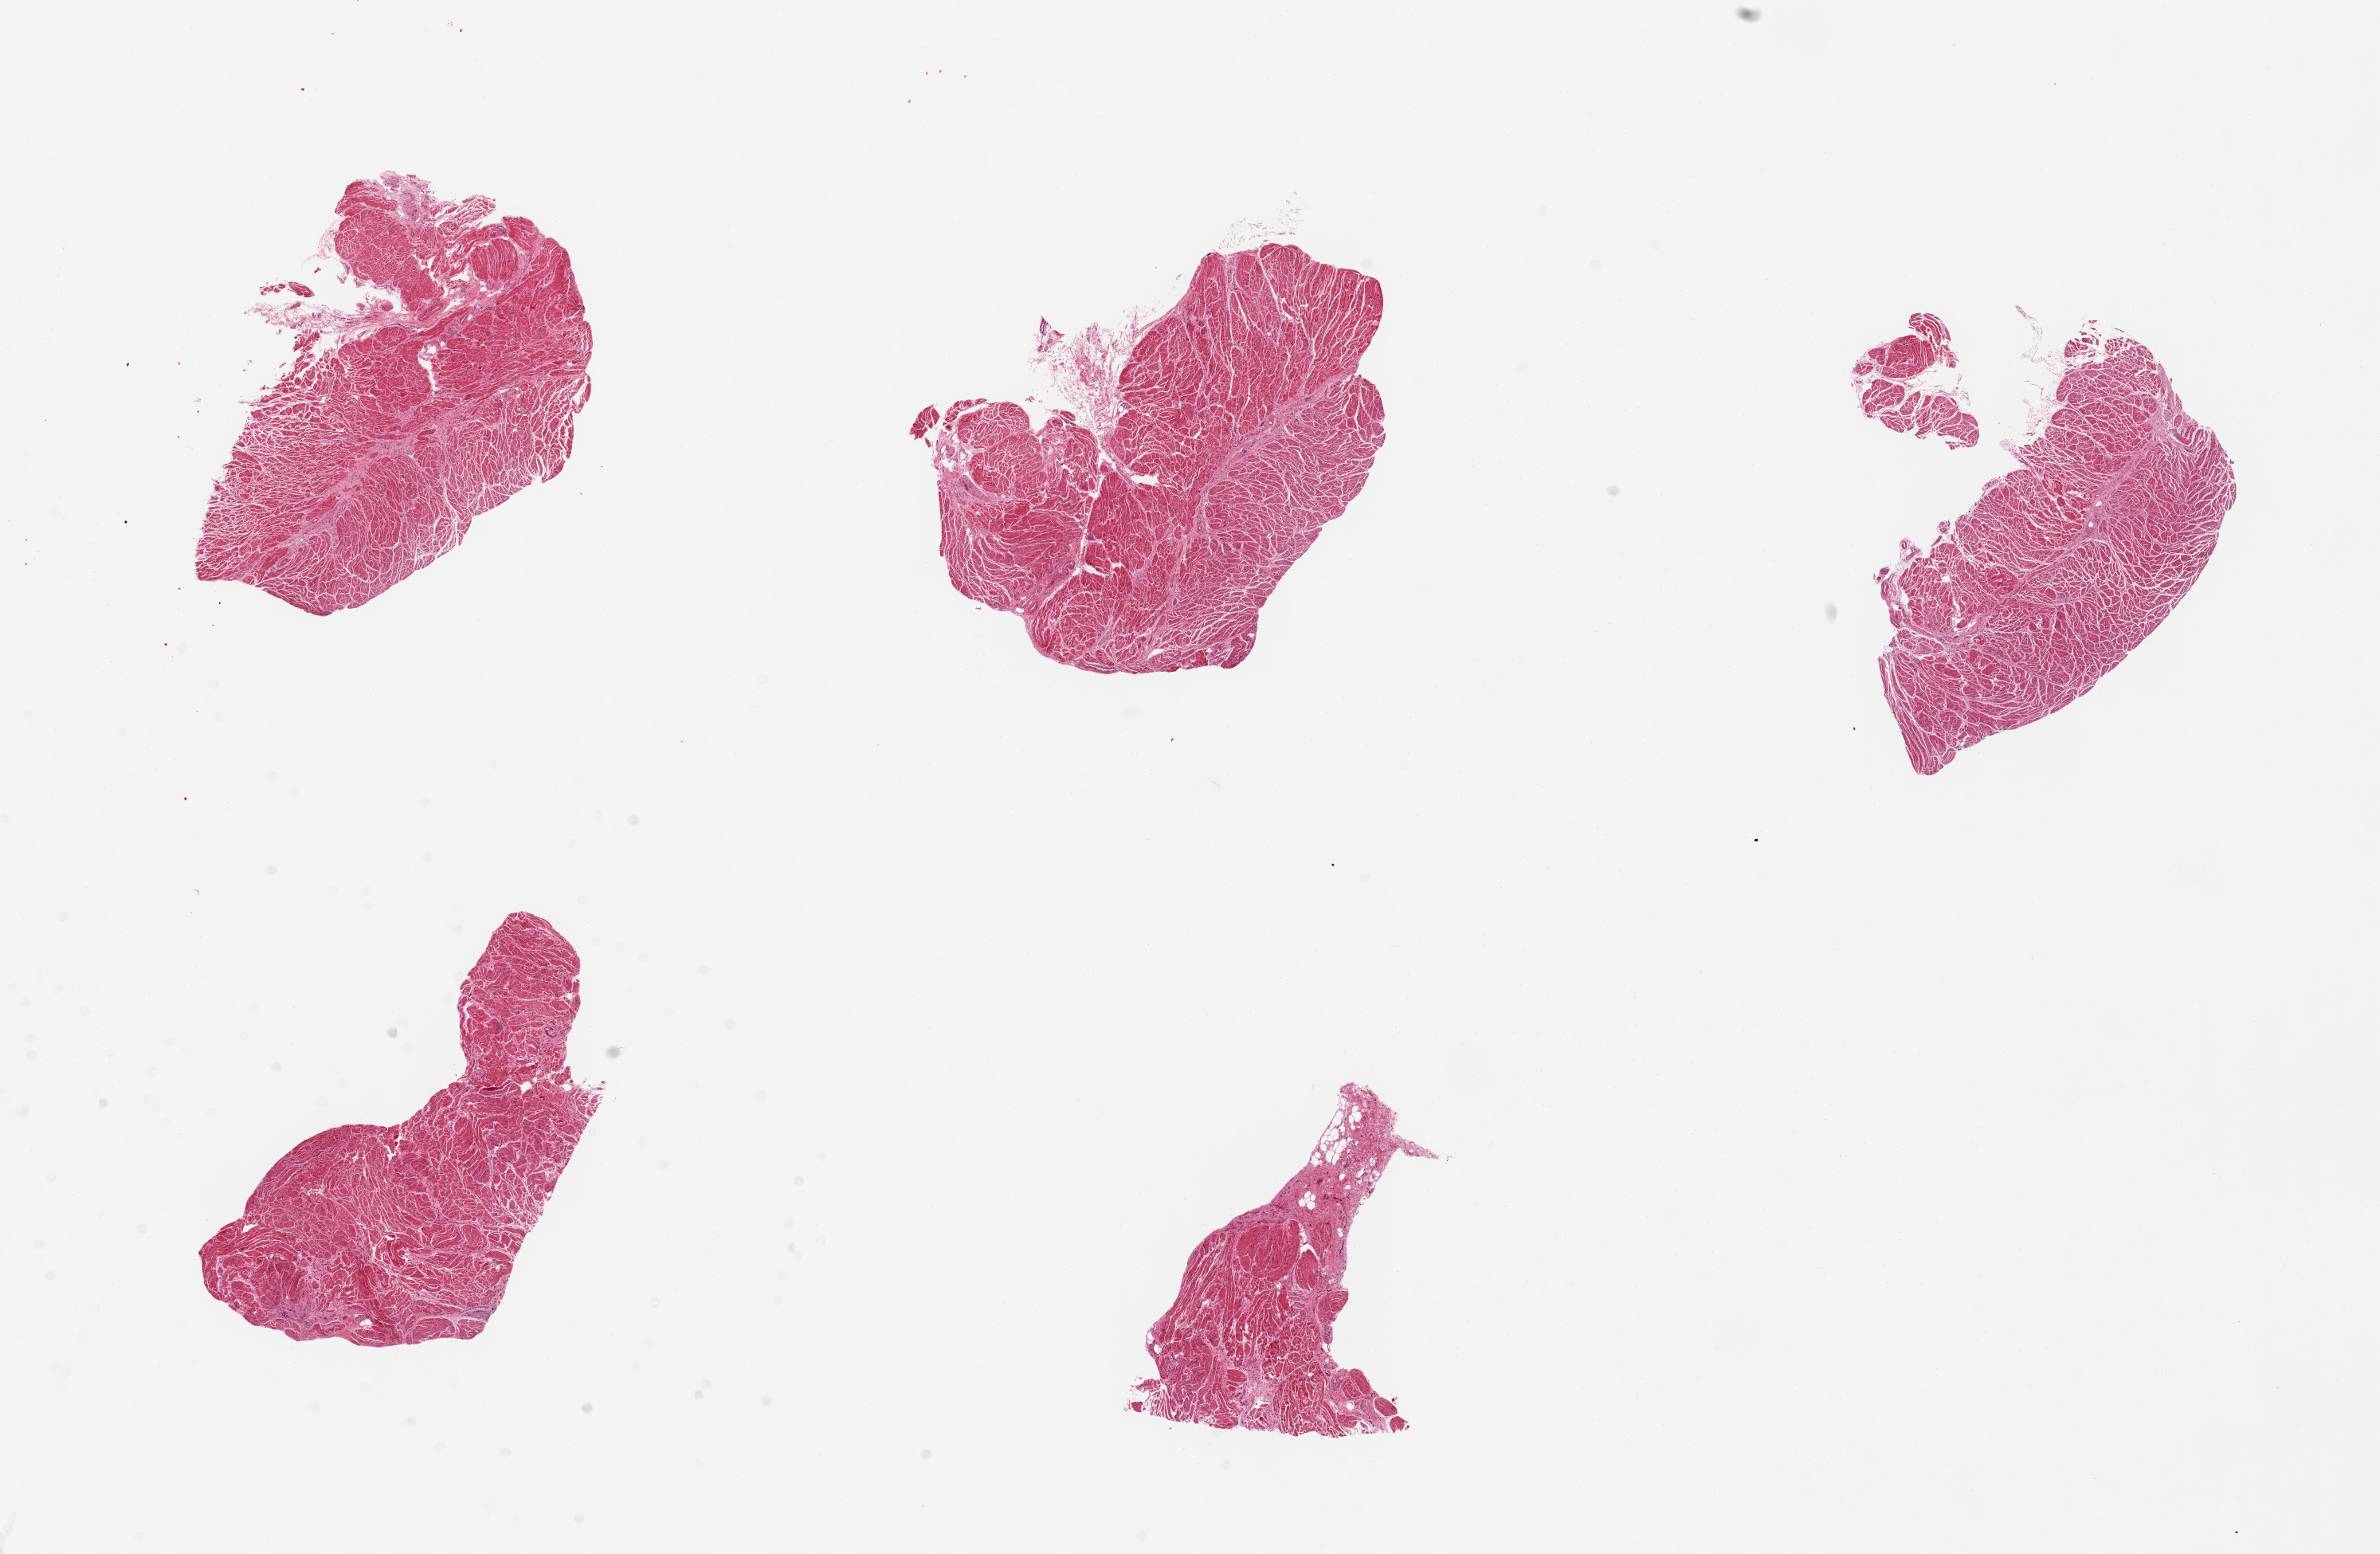
Whole-slide image, hematoxylin and eosin (H&E) stain, brightfield — shown as a low-resolution overview of the whole scanned area (about 23.6 x 15.4 mm, slide scanned at 20x); PAXgene-fixed paraffin-embedded (PFPE) section; section of esophageal muscle (target tissue); tissue donor sample. Donor sex: male.
• pathologist's review note for this sample: 5 pieces; well trimmed muscle